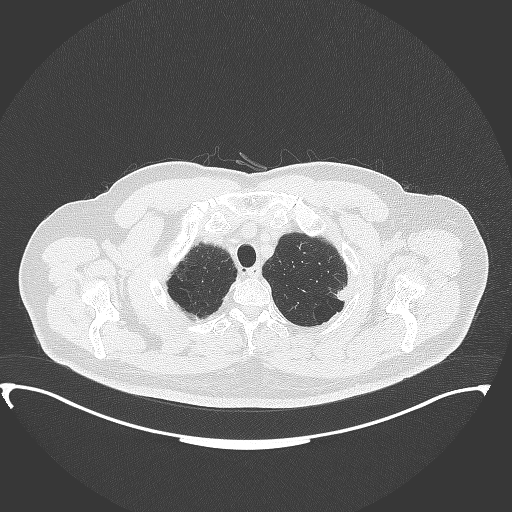
Chest CT, one axial slice; slice 328 of 350 in the series (ordered by position); reconstruction kernel B70f; lung window (W 1500 / L -600 HU); 1 mm slice thickness; 512 × 512 image matrix, field of view 459 × 459 mm. Patient: male, 64 years. From the clinical record (not read from this slice): clinical TNM (as recorded): T1c N1 M1.
Structures marked on this image (bounding box drawn by a radiologist):
- lung tumour (recorded histology: adenocarcinoma): bounding box [x1, y1, x2, y2] px = [327, 280, 355, 310]